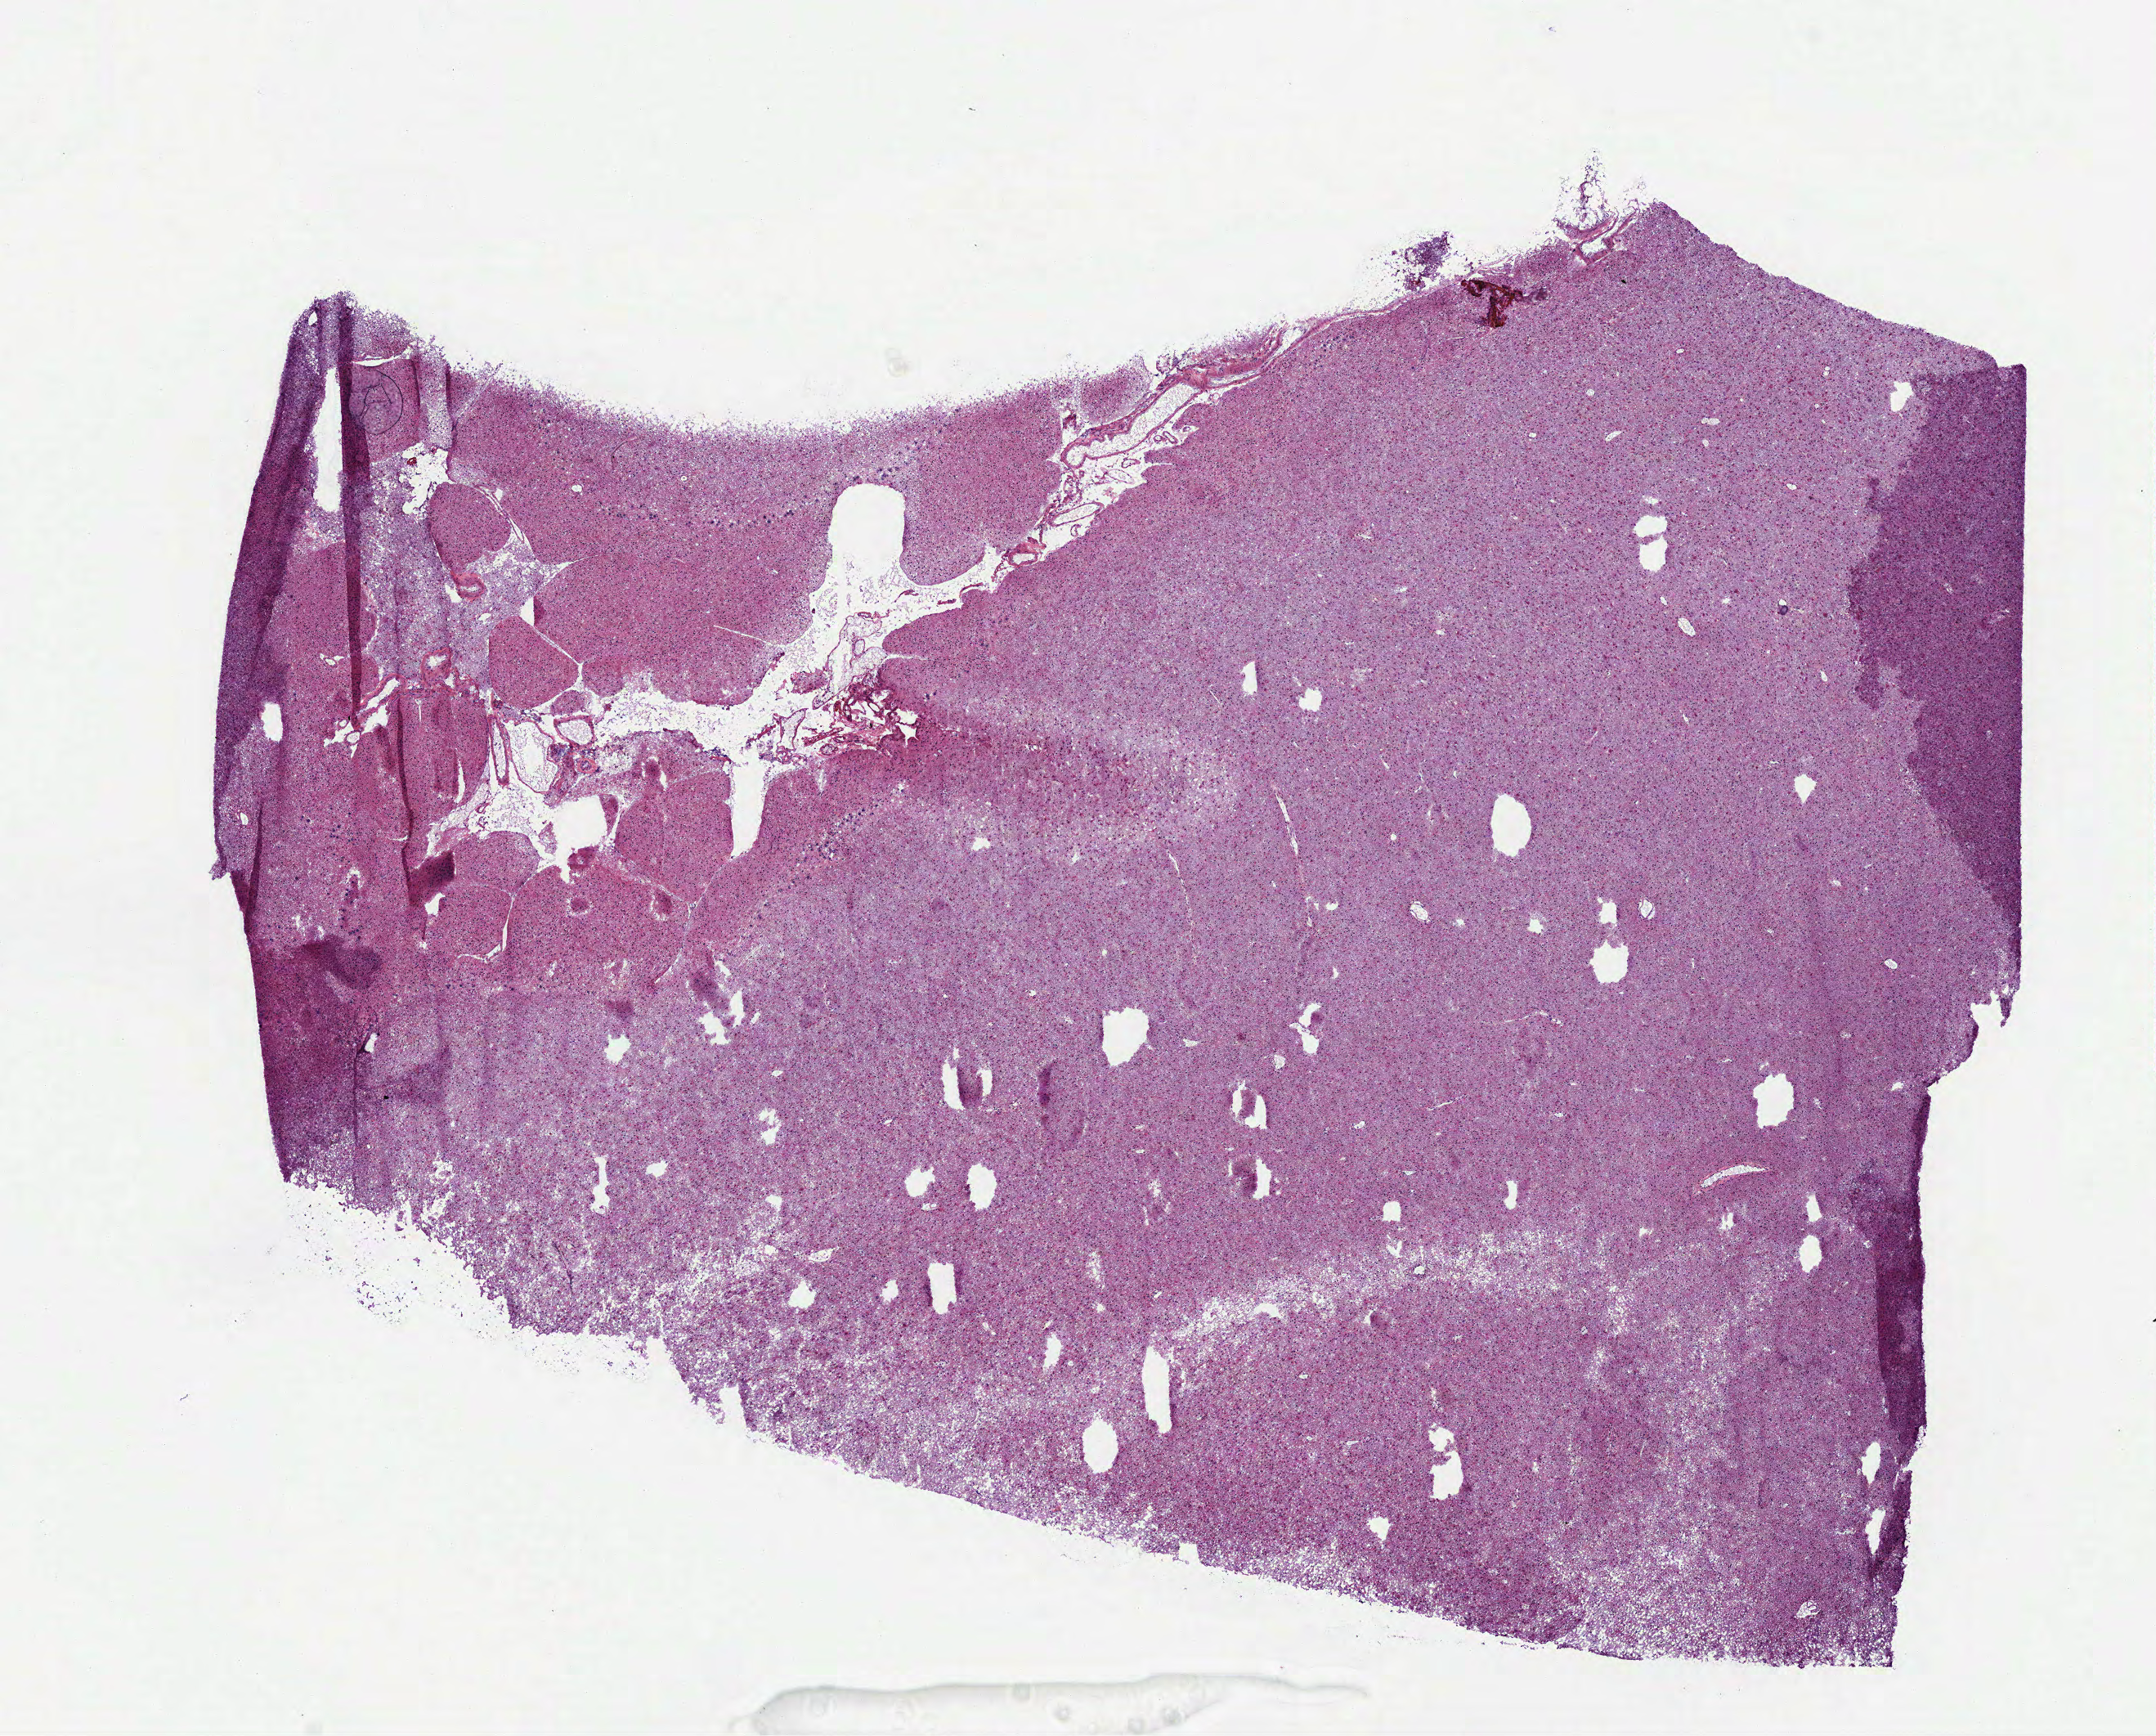
Digitized H&E tissue section (whole slide), low-resolution overview of the scanned area, about 10.6 x 8.6 mm, frozen section from the top of the tissue portion, sample: primary tumour, brain. Patient: male, age at initial diagnosis 62 years. Histologic grade: G2 (moderately differentiated). Slide review estimates, as recorded: tumour cells 95%, tumour nuclei 75%, normal cells 0%, stromal cells 5%, necrosis 0%.
Histologic diagnosis: Astrocytoma, NOS (cerebrum). Laterality: left.